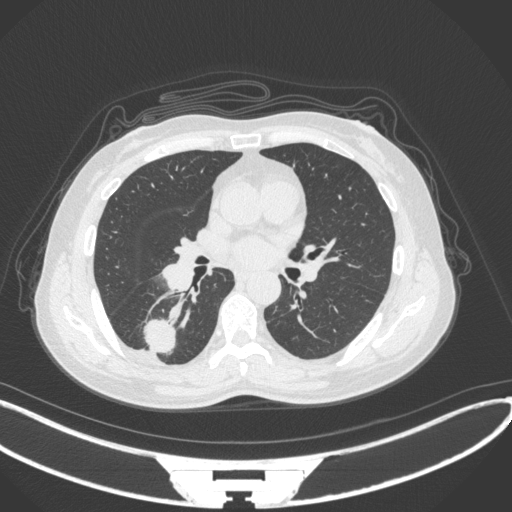
Chest CT, one axial slice; position 159 of 352 along the scan axis; 120 kVp; lung window (W 1500 / L -600 HU); 1 mm slice thickness; 512 × 512 image matrix, field of view 400 × 400 mm. Patient: female, 55 years. Case-level facts recorded for this patient, not image findings: clinical TNM (as recorded): T1c N1 M0.
Outlined on this slice (rectangle marked by the reading radiologist):
- lung tumour (recorded histology: adenocarcinoma): bounding box <140,316,180,359> (left, top, right, bottom; pixels)